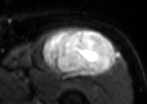
MRI of an extremity soft-tissue mass, one axial slice; position 63 of 85 along the scan axis; T2-weighted fat-saturated; MR volume resampled by the dataset authors to the PET/CT grid (not the native acquisition matrix); 3.27 mm slice thickness; 147 × 104 image matrix. Male patient. From the clinical record (not read from this slice): histological type: extraskeletal osteosarcoma; grade: high; site of the primary tumour: thigh.
Annotated regions visible in this slice (expert contour drawn on MRI and transferred to this co-registered scan by the dataset authors):
- gross tumour volume (mass): box from (x=42, y=28) to (x=116, y=77) px